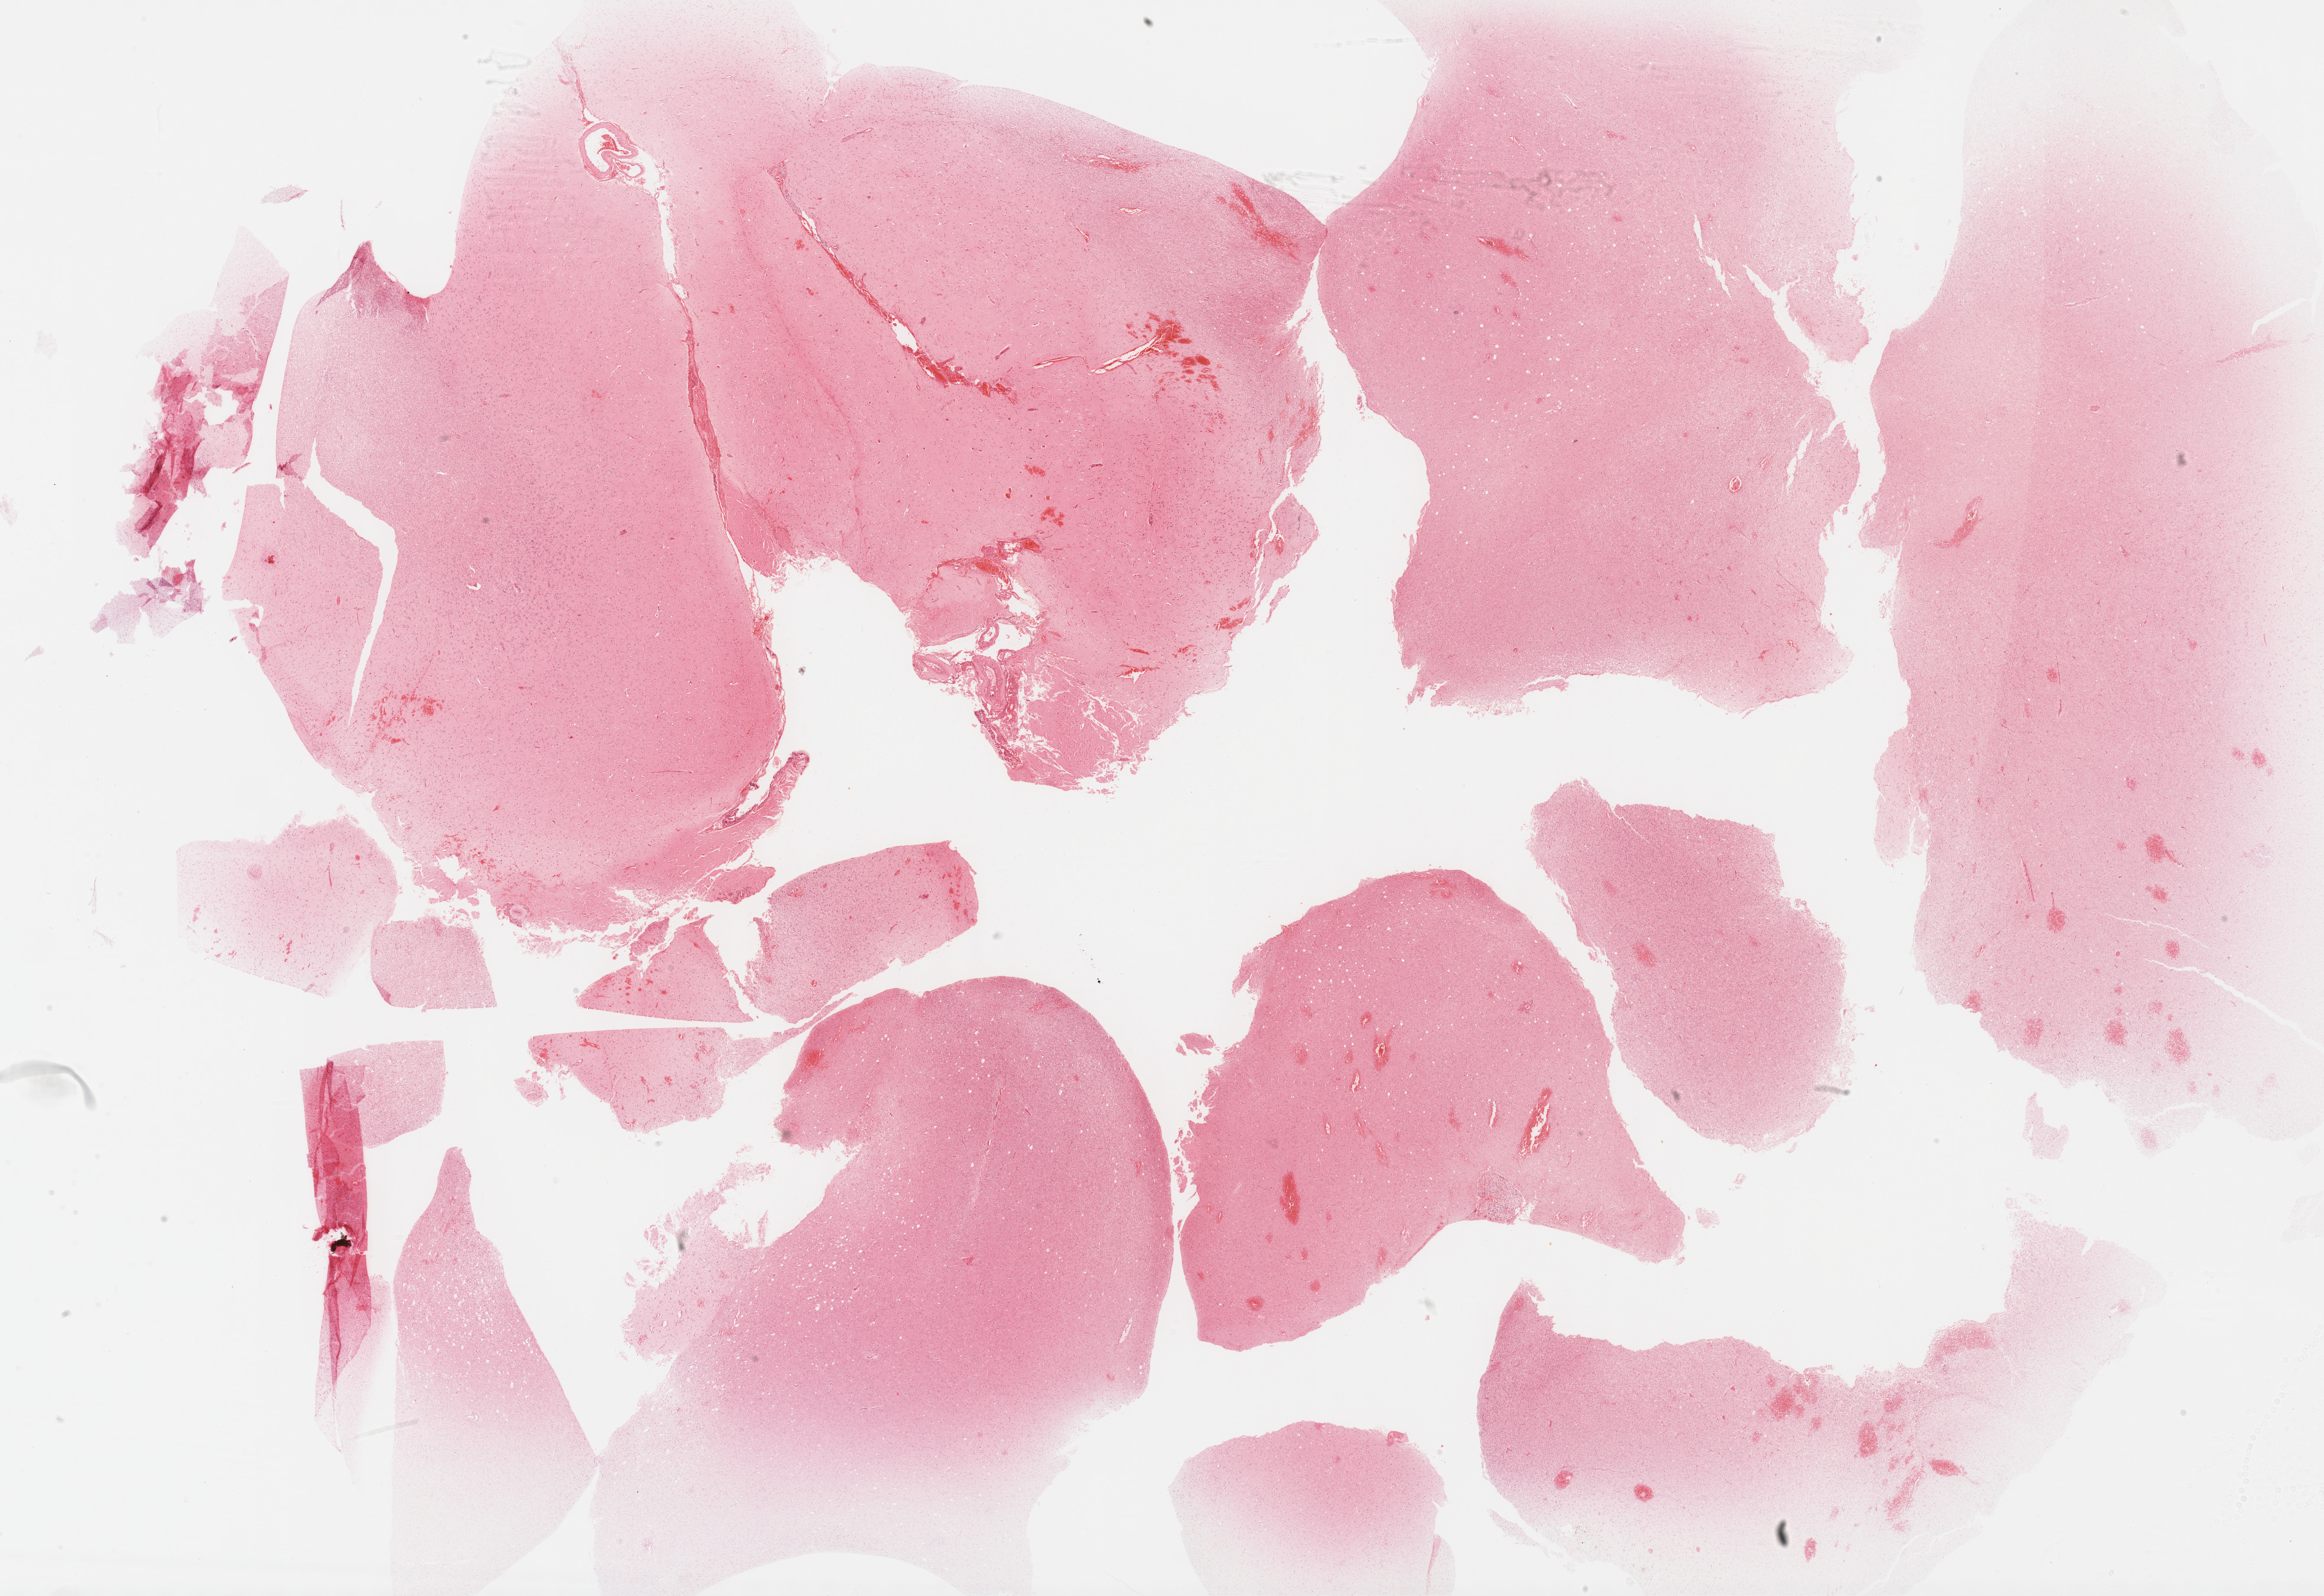
Whole-slide histology image, H&E-stained, shown as a low-resolution overview of the whole scanned area (about 31.7 x 21.8 mm, from a 40x scan). Formalin-fixed paraffin-embedded (FFPE) diagnostic section. Primary tumour sample from the brain. Male patient; age at initial diagnosis 52 years. Histologic grade: G2 (moderately differentiated).
Diagnosis: Oligodendroglioma, NOS (cerebrum).